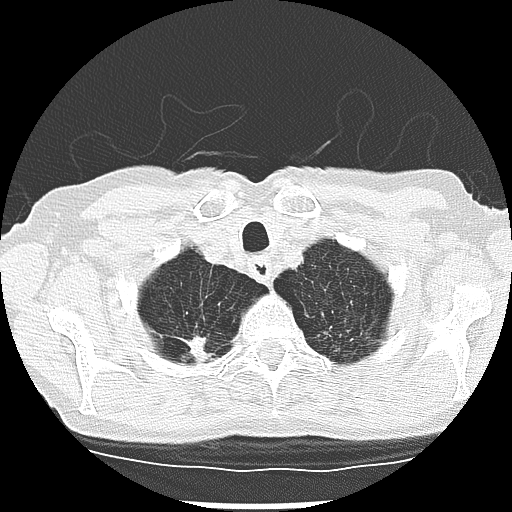
Low-dose screening chest CT, one axial slice; position 244 of 265 along the scan axis; reconstruction kernel LUNG; 120 kVp; lung window (W 1500 / L -600 HU); 2.5 mm slice thickness; 512 × 512 image matrix, field of view 300 × 300 mm.
Outlined on this slice (expert manual segmentation):
- lesion 2 (tumor, upper lobe of right lung): bounding box [x1, y1, x2, y2] px = [186, 336, 207, 360]